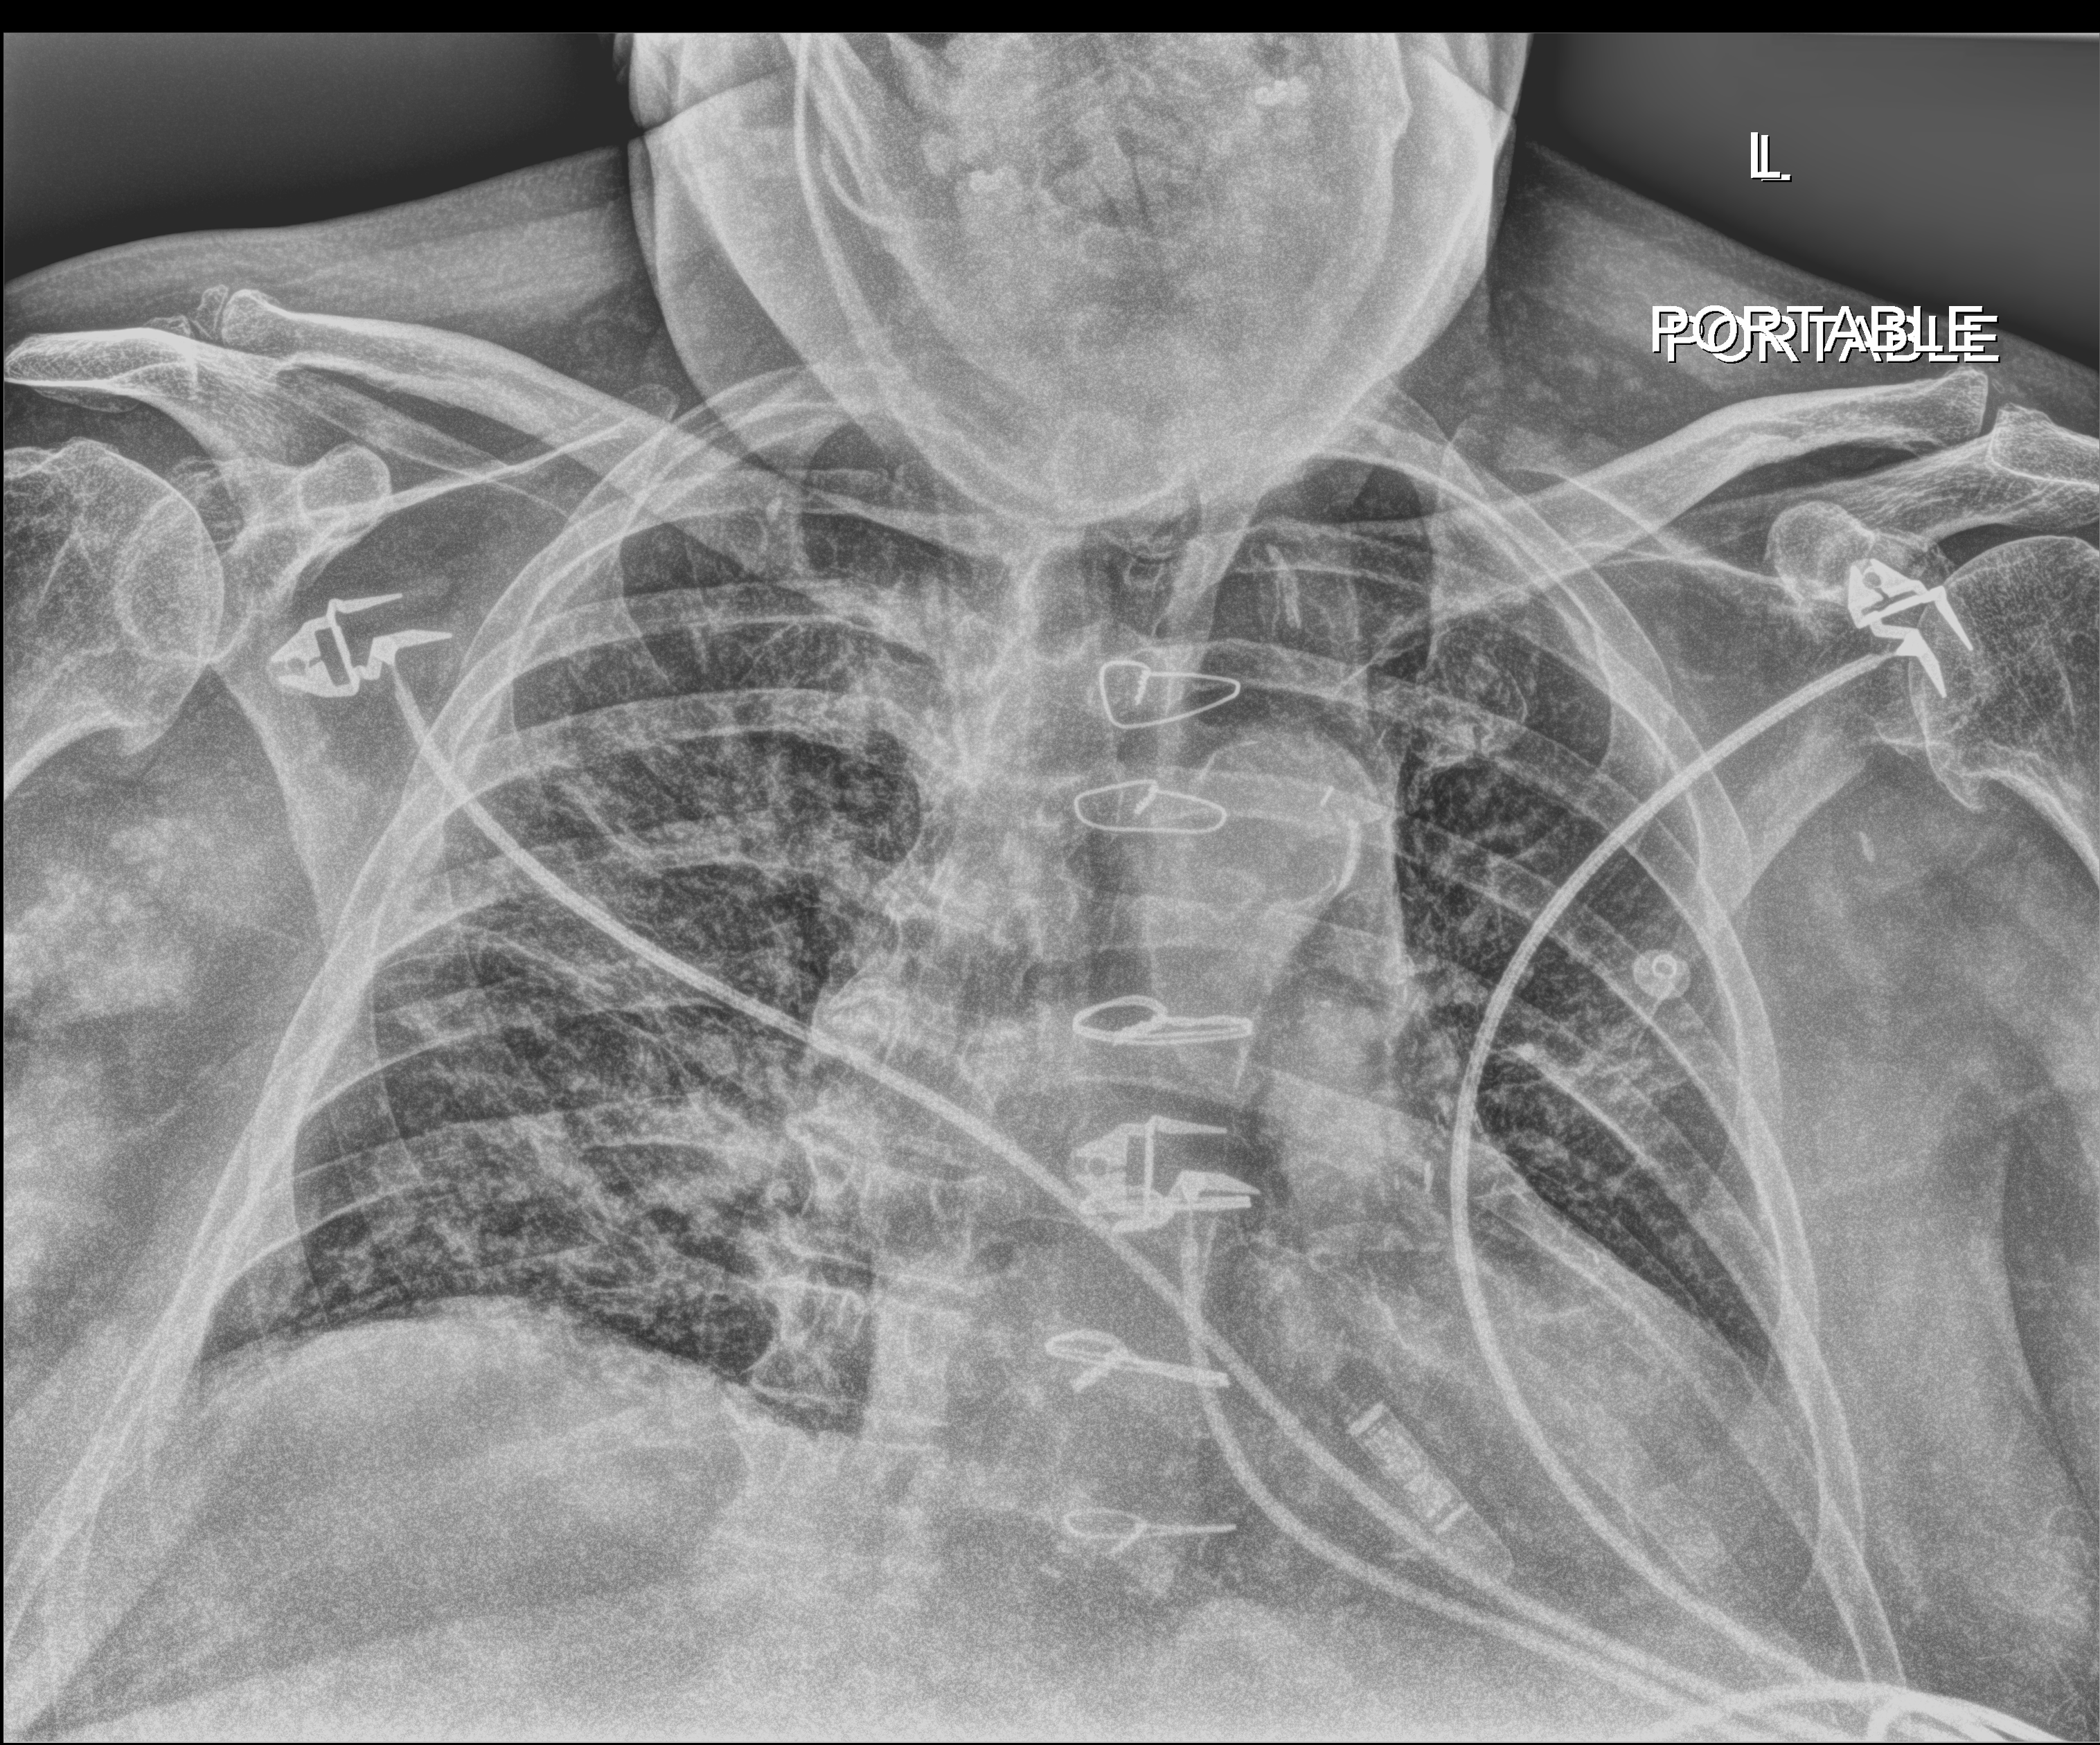
Bedside chest radiograph (digital radiography), anteroposterior (AP) projection. Male patient hospitalised with COVID-19, age 60–74 years.
Admission-level facts for this patient (not findings on this image; timing relative to this image not recorded): admitted to intensive care during this hospital stay: no.